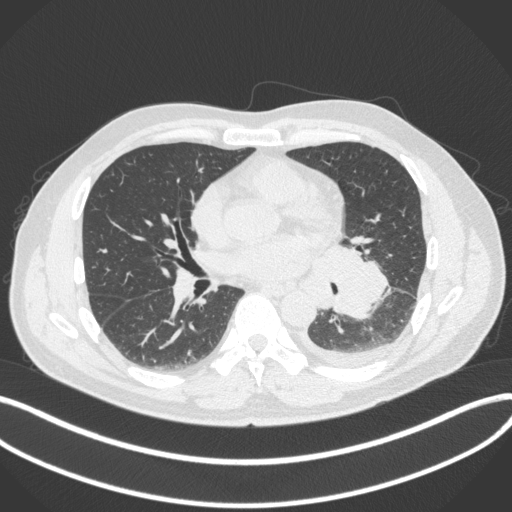
Chest CT, one axial slice. Position 177 of 350 along the scan axis. Reconstruction kernel B31f. Lung window (W 1500 / L -600 HU). 512 × 512 image matrix, field of view 400 × 400 mm. Male patient, age 58 years. From the clinical record (not read from this slice): clinical TNM (as recorded): T3 N1 M1b.
Annotated regions visible in this slice (rectangle marked by the reading radiologist):
- lung tumour (recorded histology: small cell carcinoma): bounding box <315,238,394,324> (left, top, right, bottom; pixels)